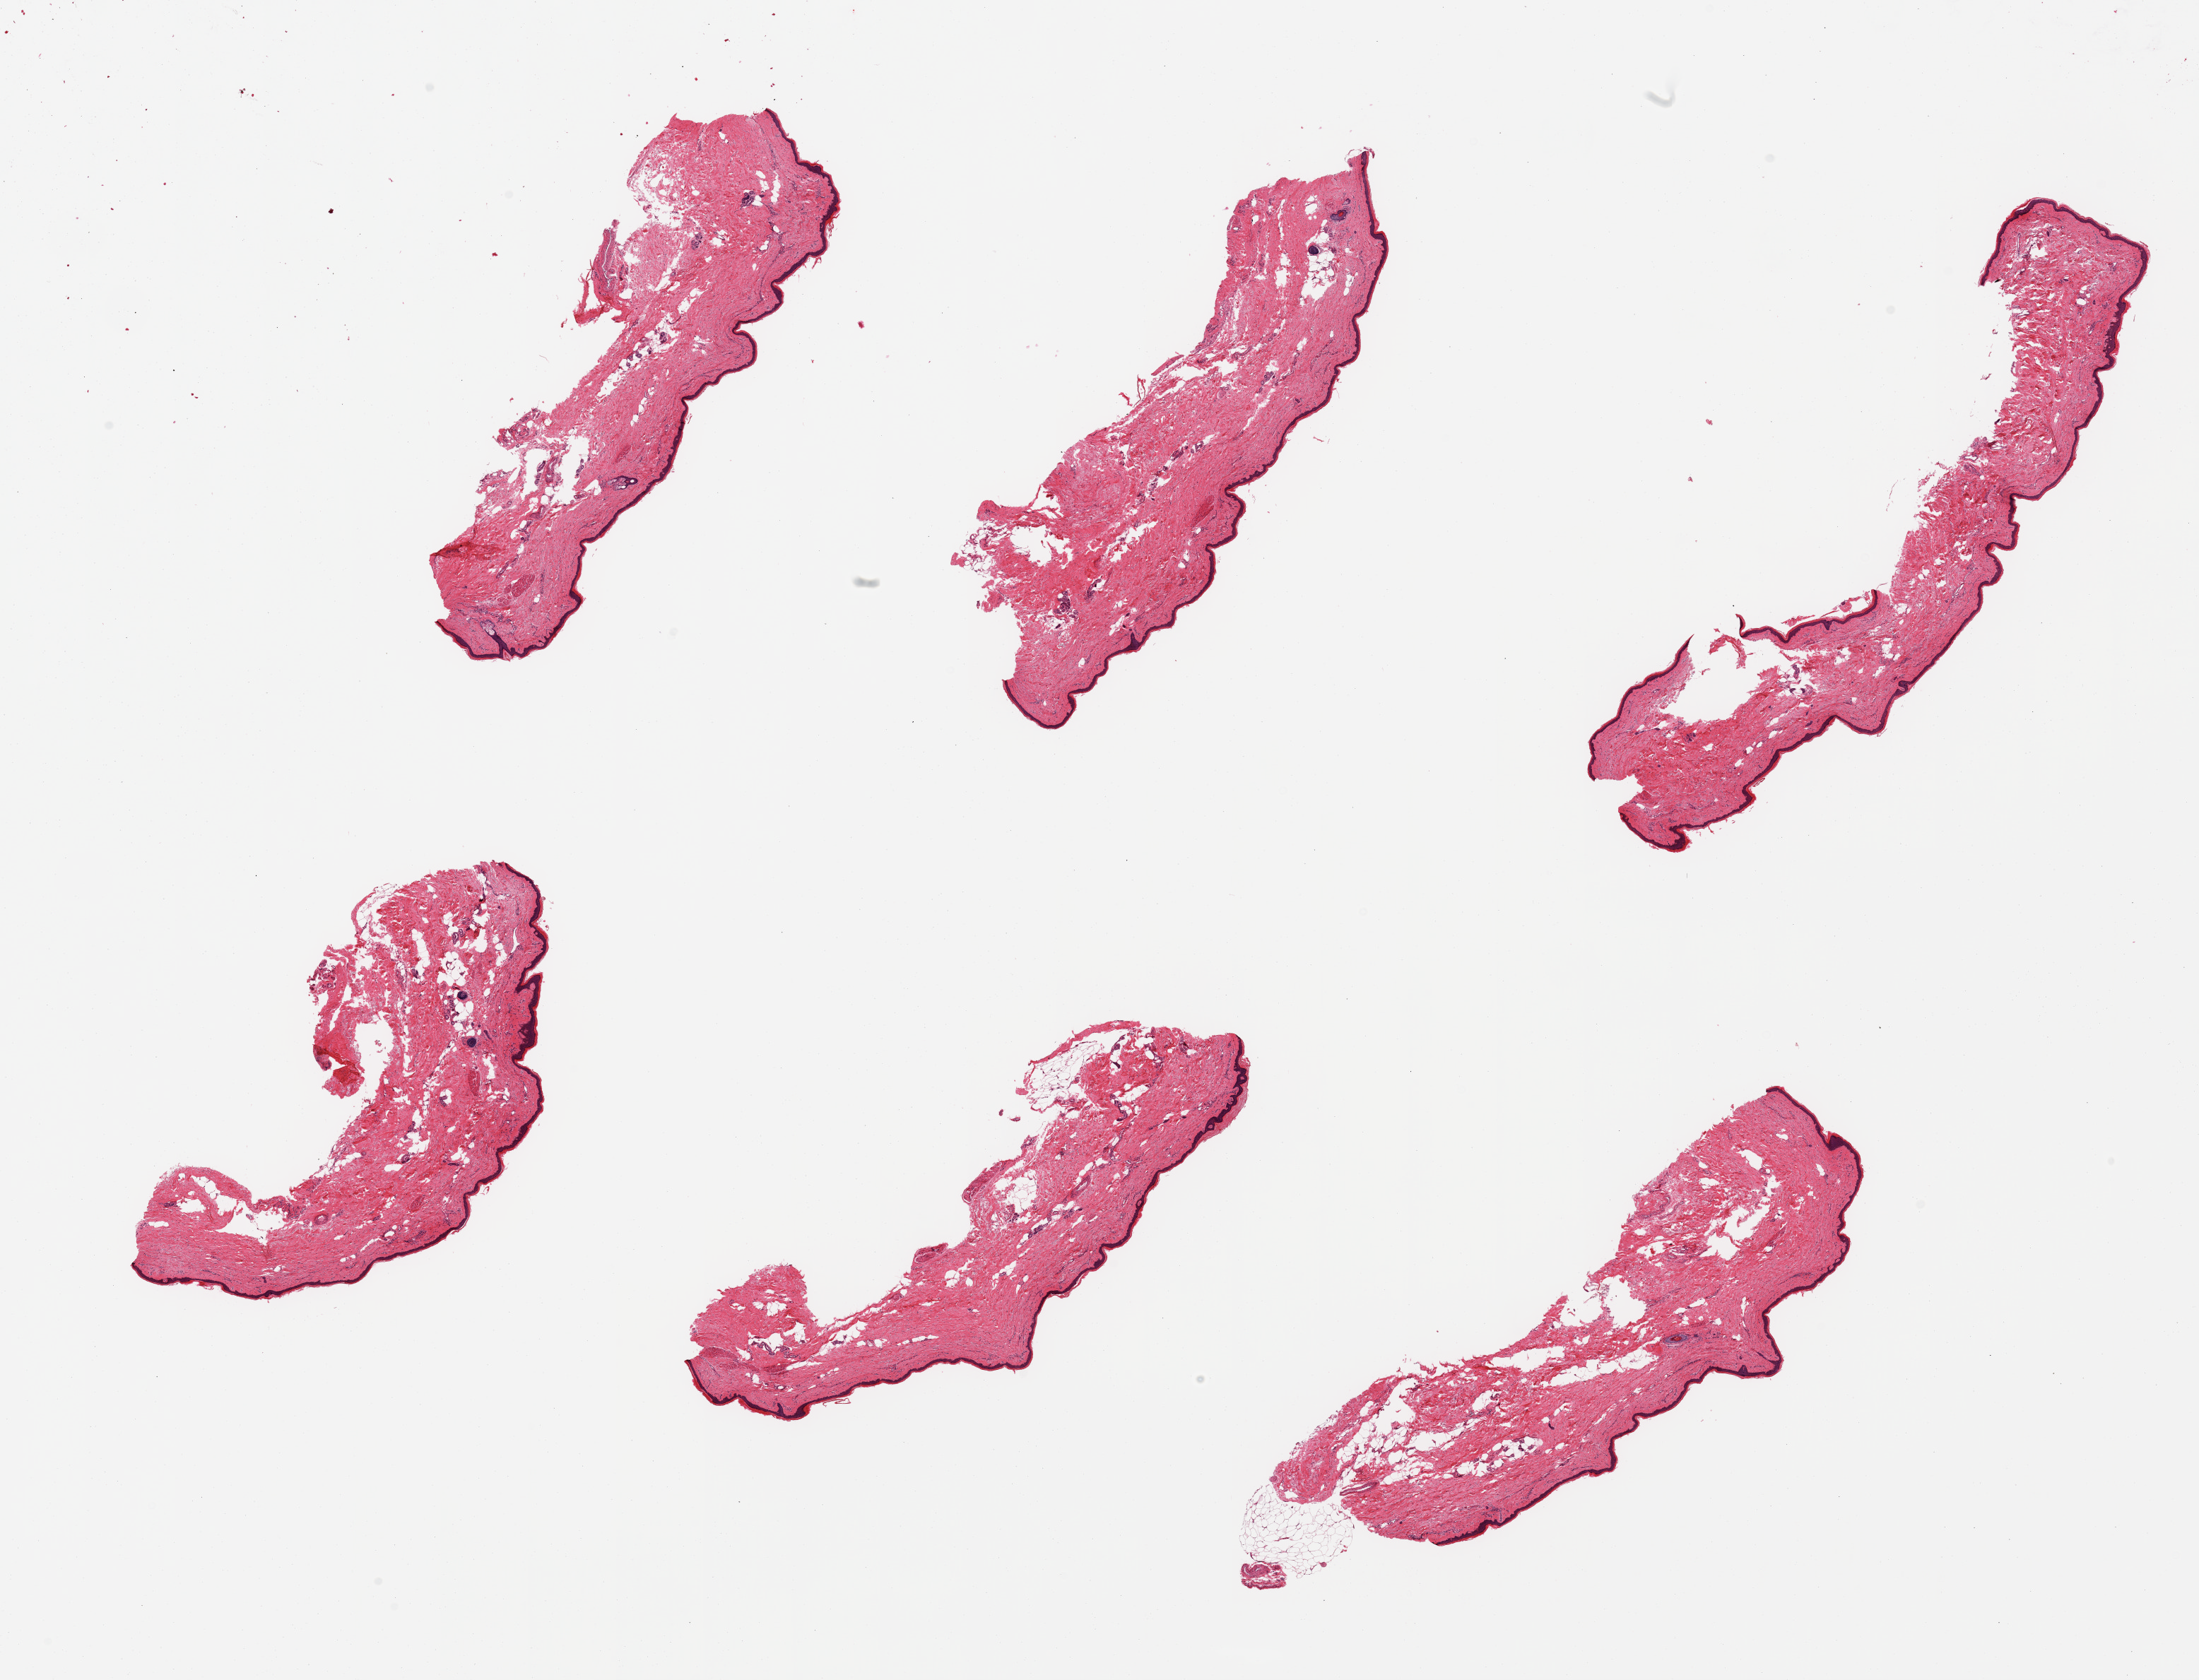
Whole-slide image, haematoxylin and eosin stain — low-resolution overview of the scanned area, about 24.6 x 18.8 mm (slide scanned at 20x). PAXgene-fixed, paraffin-embedded tissue. Sampled site (target tissue): skin of lower leg. Donor tissue sample. Donor sex: female.
- review note (as recorded): 6 pieces; well trimmed; 10% dermal fat; dermal fragmentation